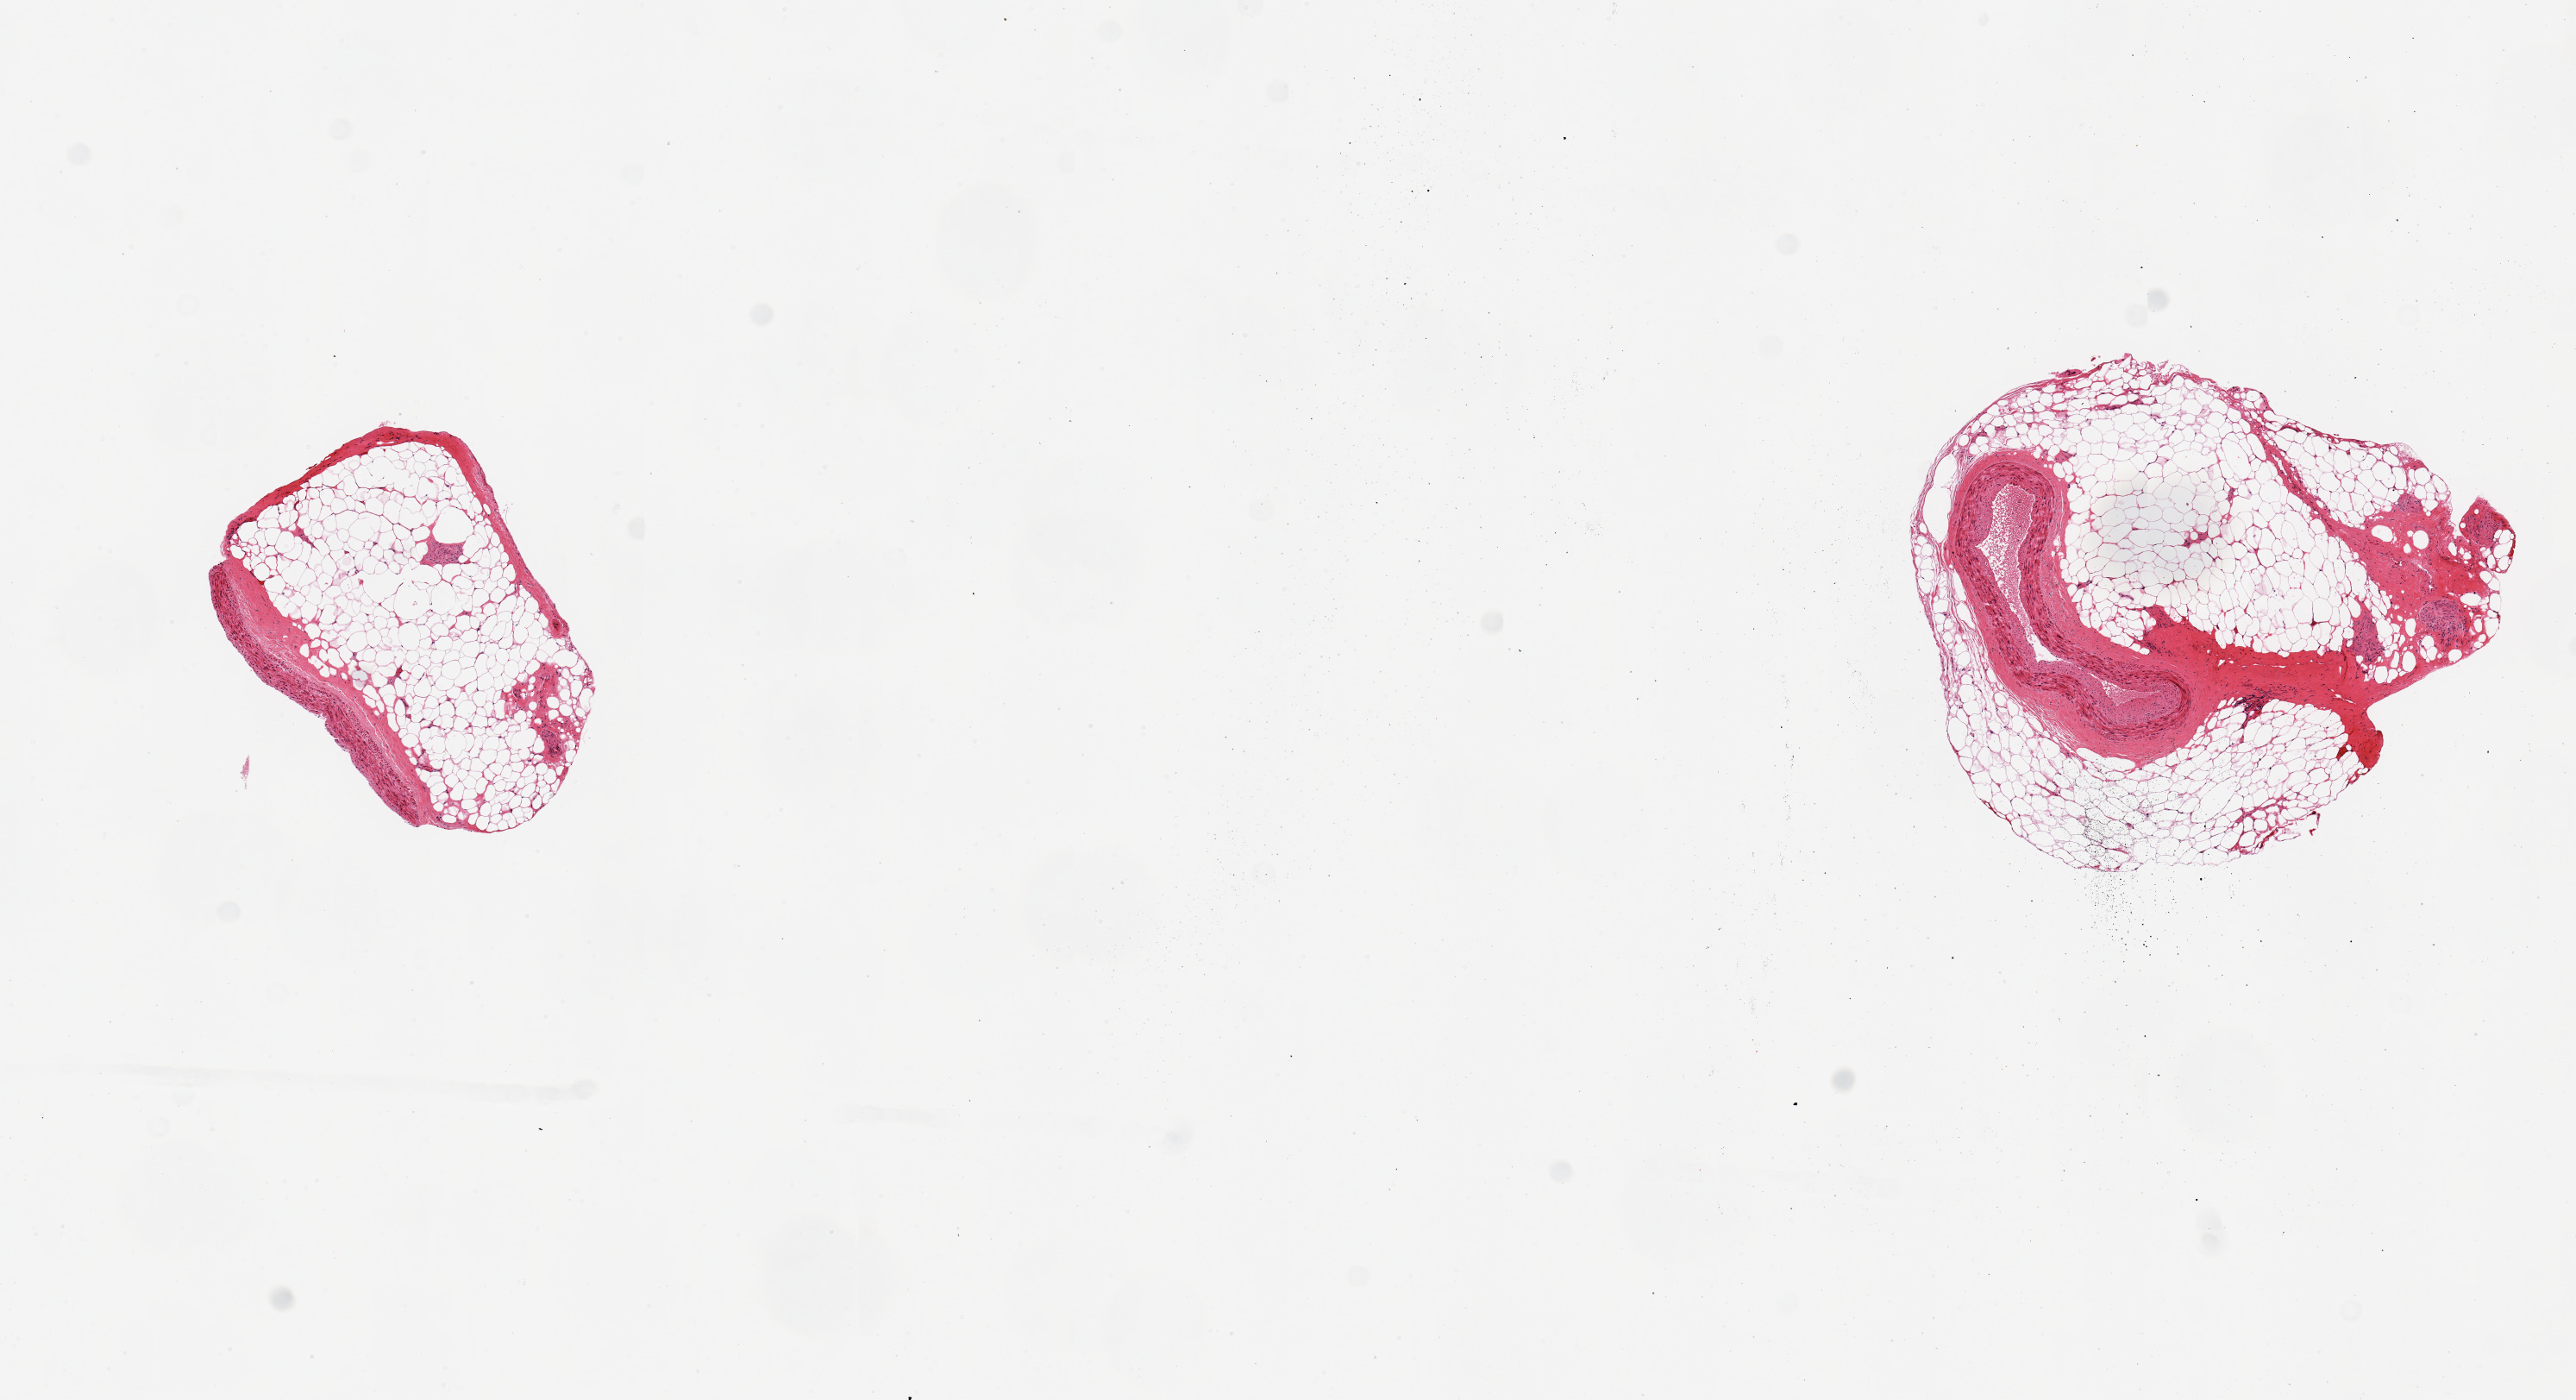
Whole-slide image, haematoxylin and eosin stain, brightfield, low-resolution overview of the scanned area, about 11.8 x 6.4 mm. PAXgene-fixed paraffin-embedded (PFPE) section. Target tissue: coronary artery. Donor tissue sample. Donor sex: male.
Reviewer comment on this tissue sample: 2 pieces, abundant attached fat (80-90%).